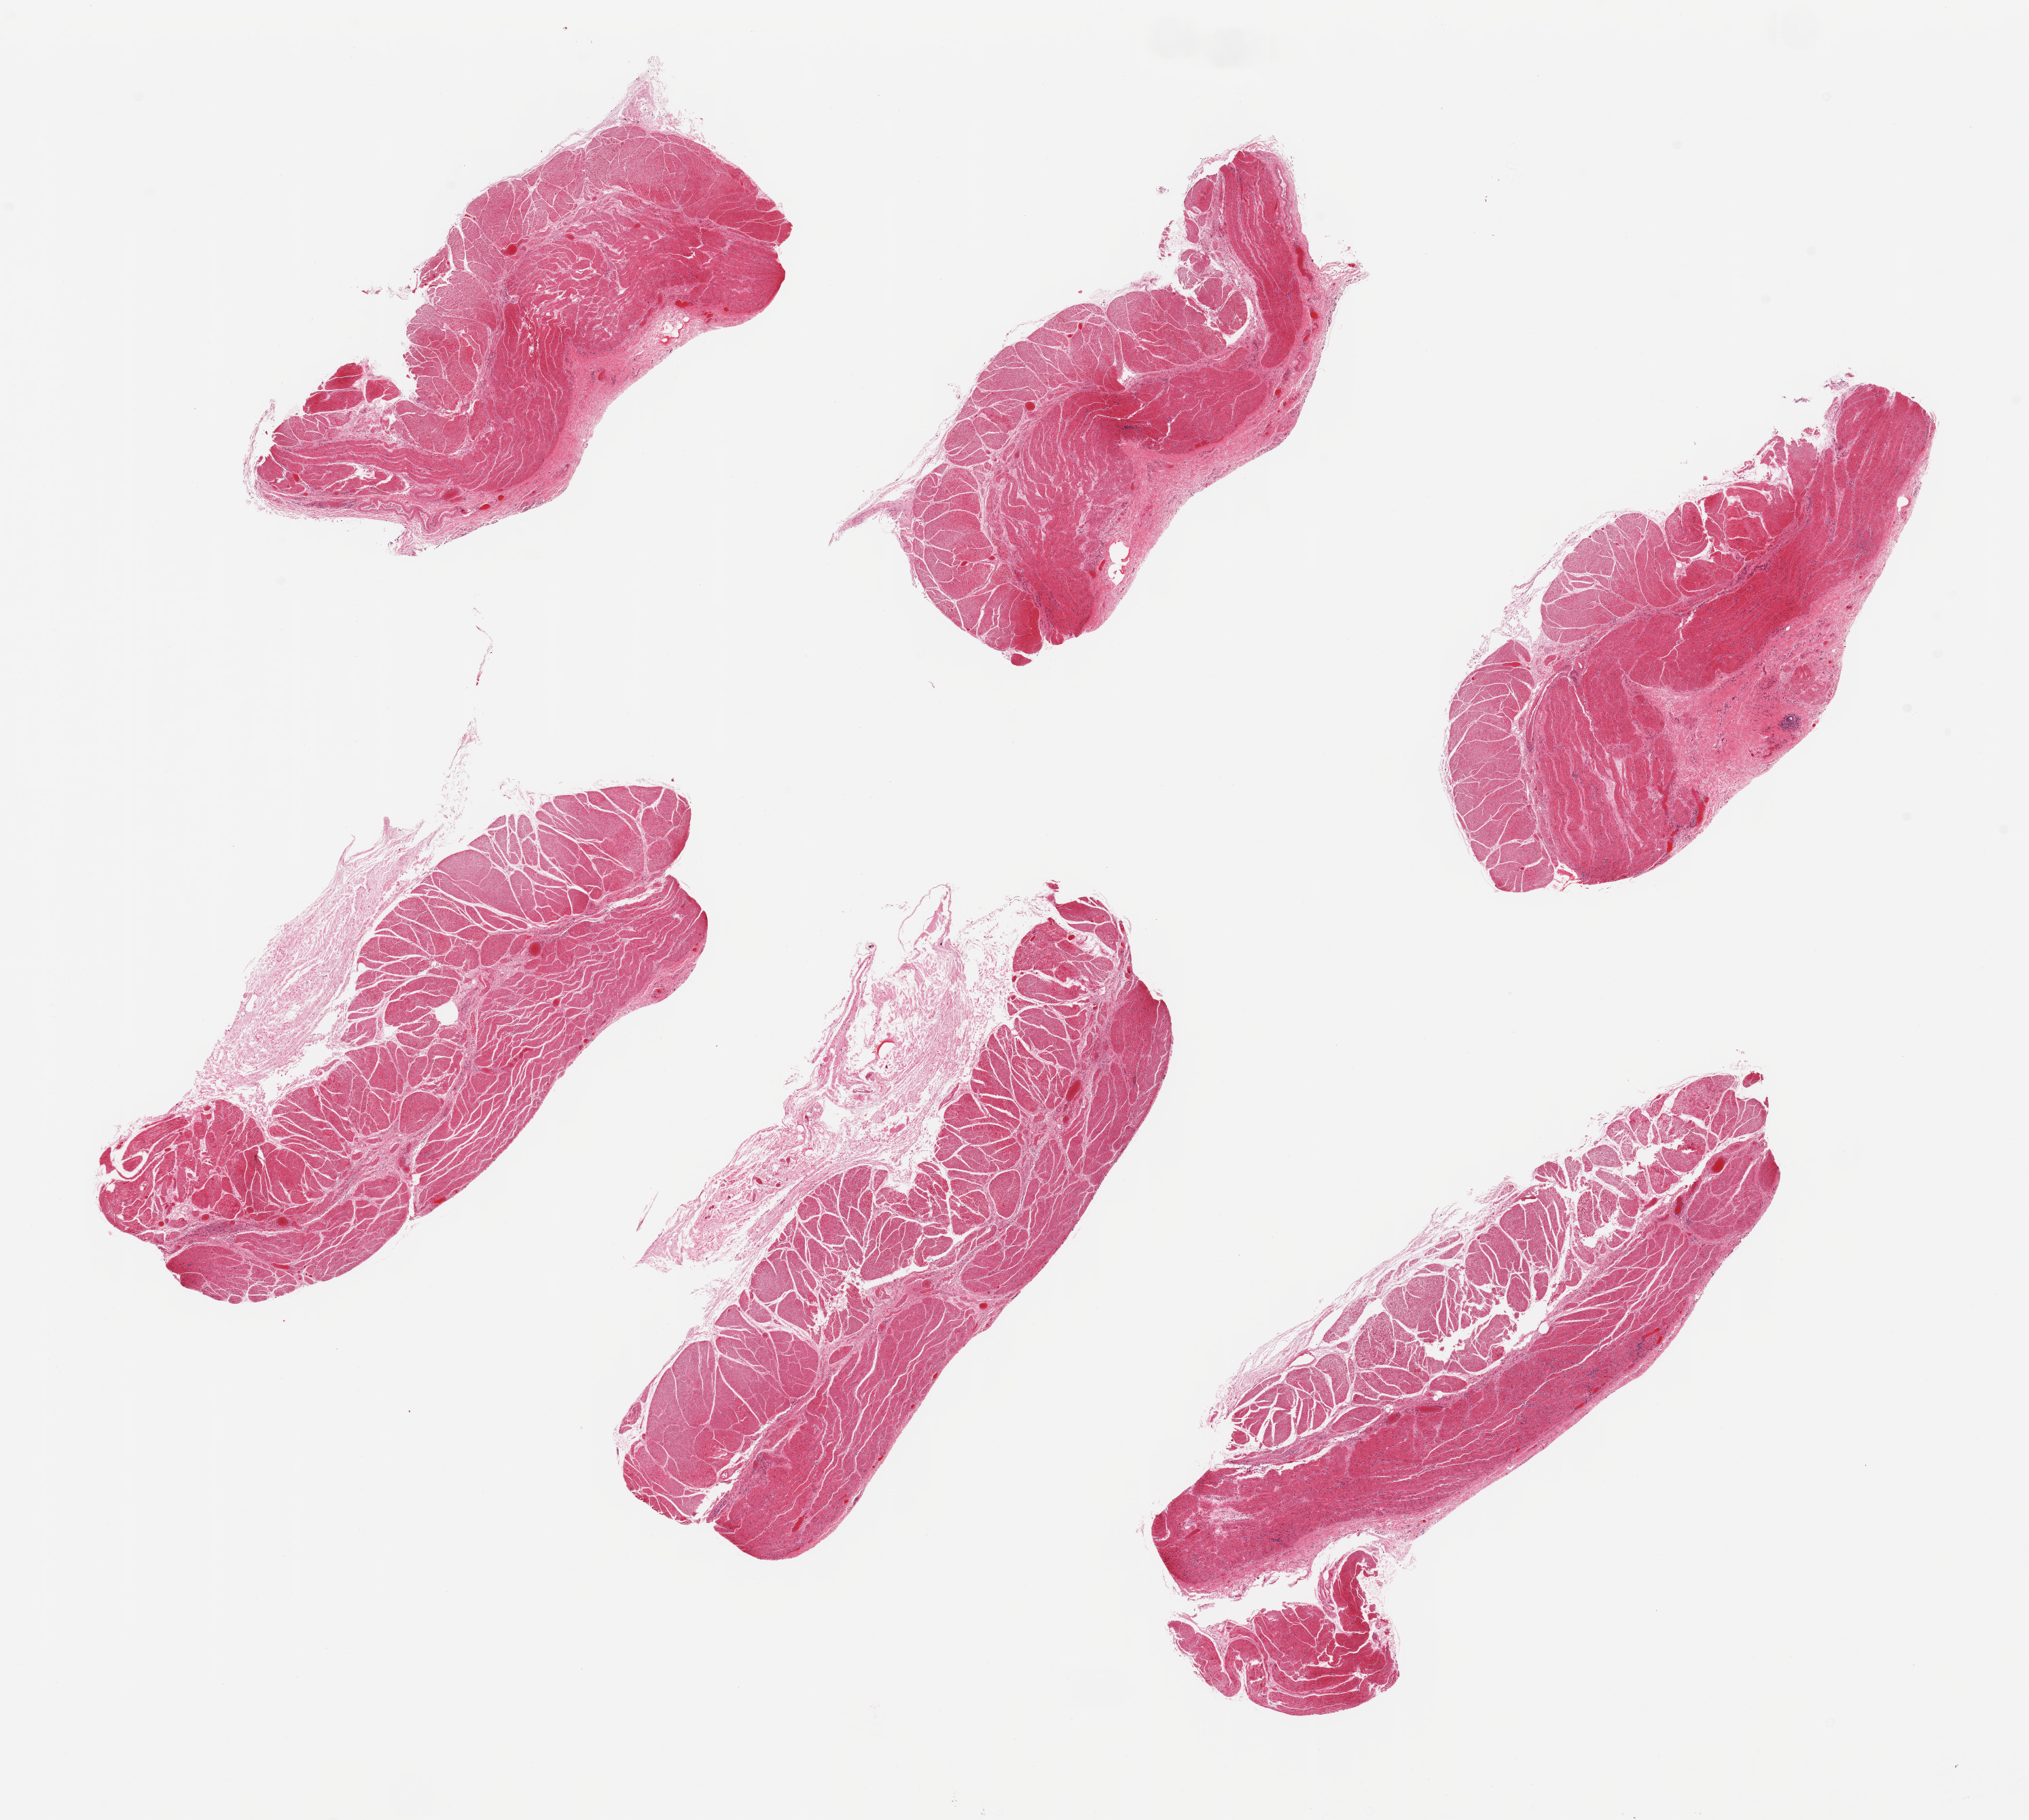
Whole-slide image, hematoxylin and eosin (H&E) stain, shown as a low-resolution overview of the whole scanned area (about 23.6 x 21.2 mm, from a 20x scan). PAXgene-fixed, paraffin-embedded tissue. Section of esophageal muscle (target tissue). Donor tissue sample. Male donor.
• pathologist's review note for this sample: 6 pieces, all muscularis, unusually autolyzed